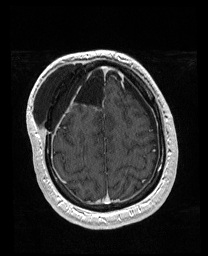
Brain MRI from a brain-tumour surgery series, one axial slice. Position 49 of 176 along the scan axis. T1-weighted post-contrast. 208 × 256 image matrix. Case-level facts recorded for this patient, not image findings: histopathology: Astrocytoma; WHO grade: 4; IDH mutation: yes; tumour location: Right Orbitofrontal Anterior Temporal Insular.
Annotated regions visible in this slice (outlined manually by an expert reader):
- previous resection cavity: bounding box (x1, y1, x2, y2) in pixels: (56, 64, 106, 106)